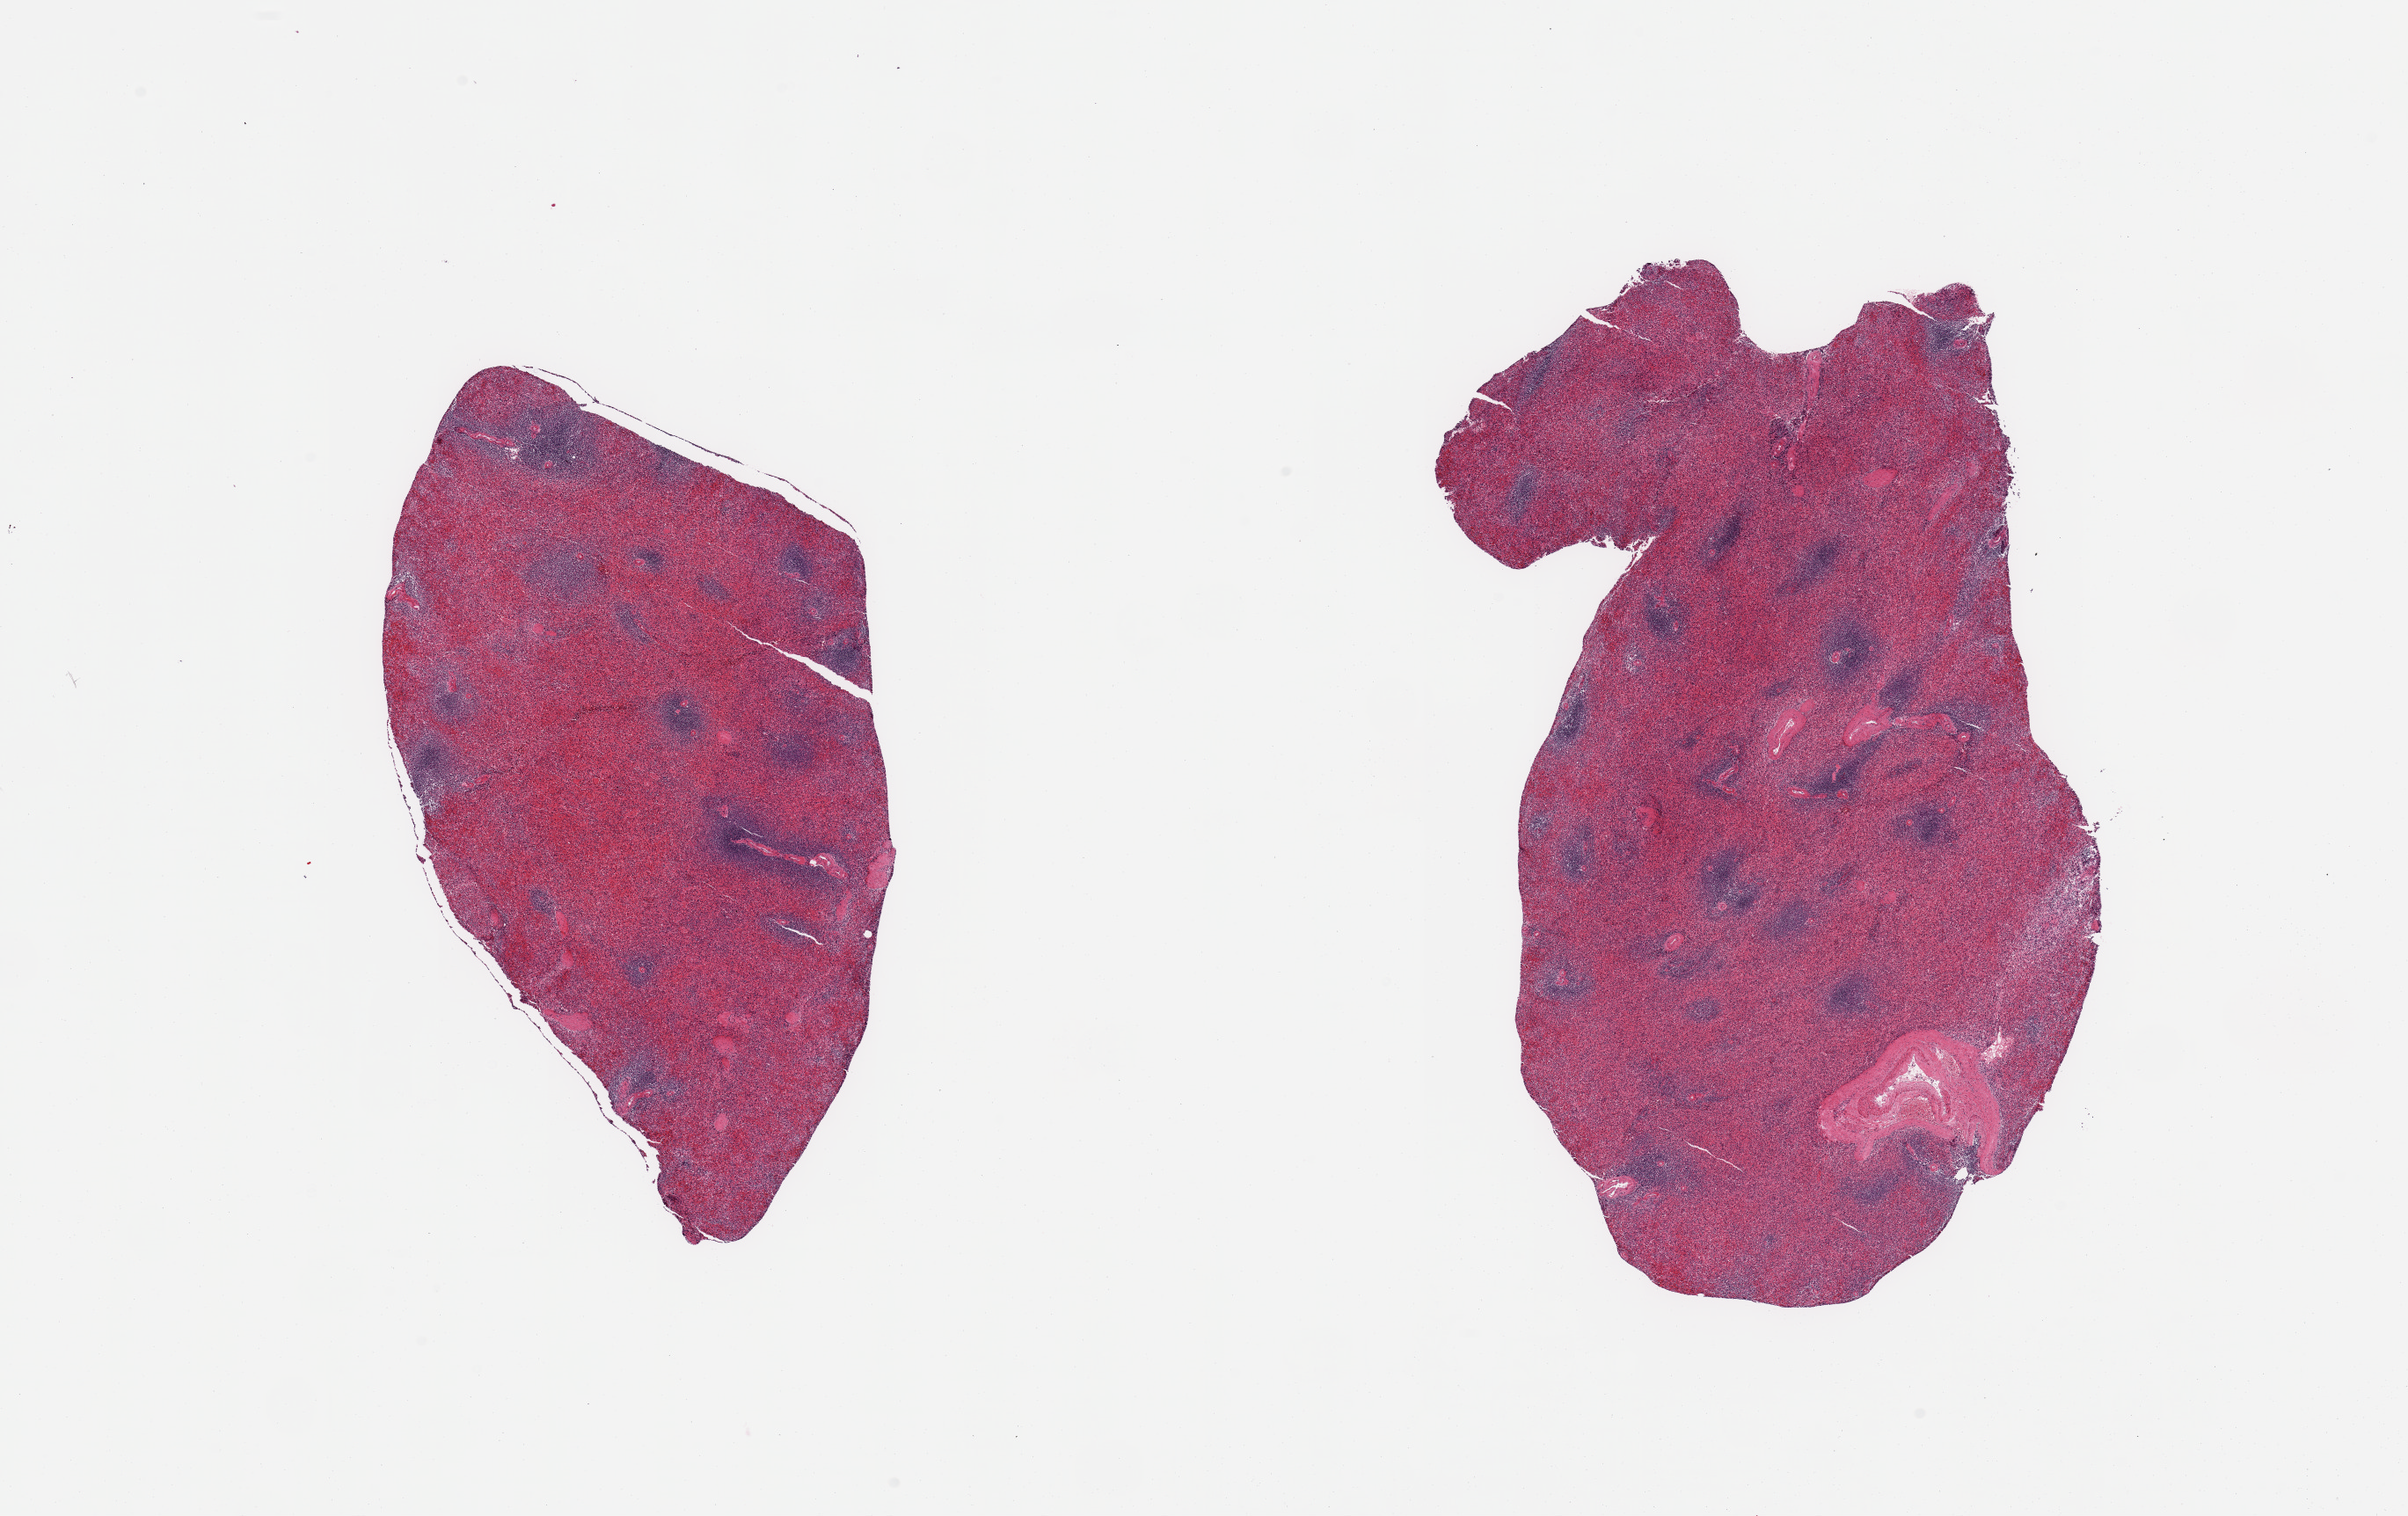
Haematoxylin and eosin whole-slide image, whole scanned area (about 21.7 x 13.6 mm, from a 20x scan) shown as a low-resolution overview. PAXgene-fixed, paraffin-embedded tissue. Sampled site (target tissue): spleen. Tissue donor sample. Donor sex: male.
- pathologist's review note for this sample: 2 pieces; moderately congested